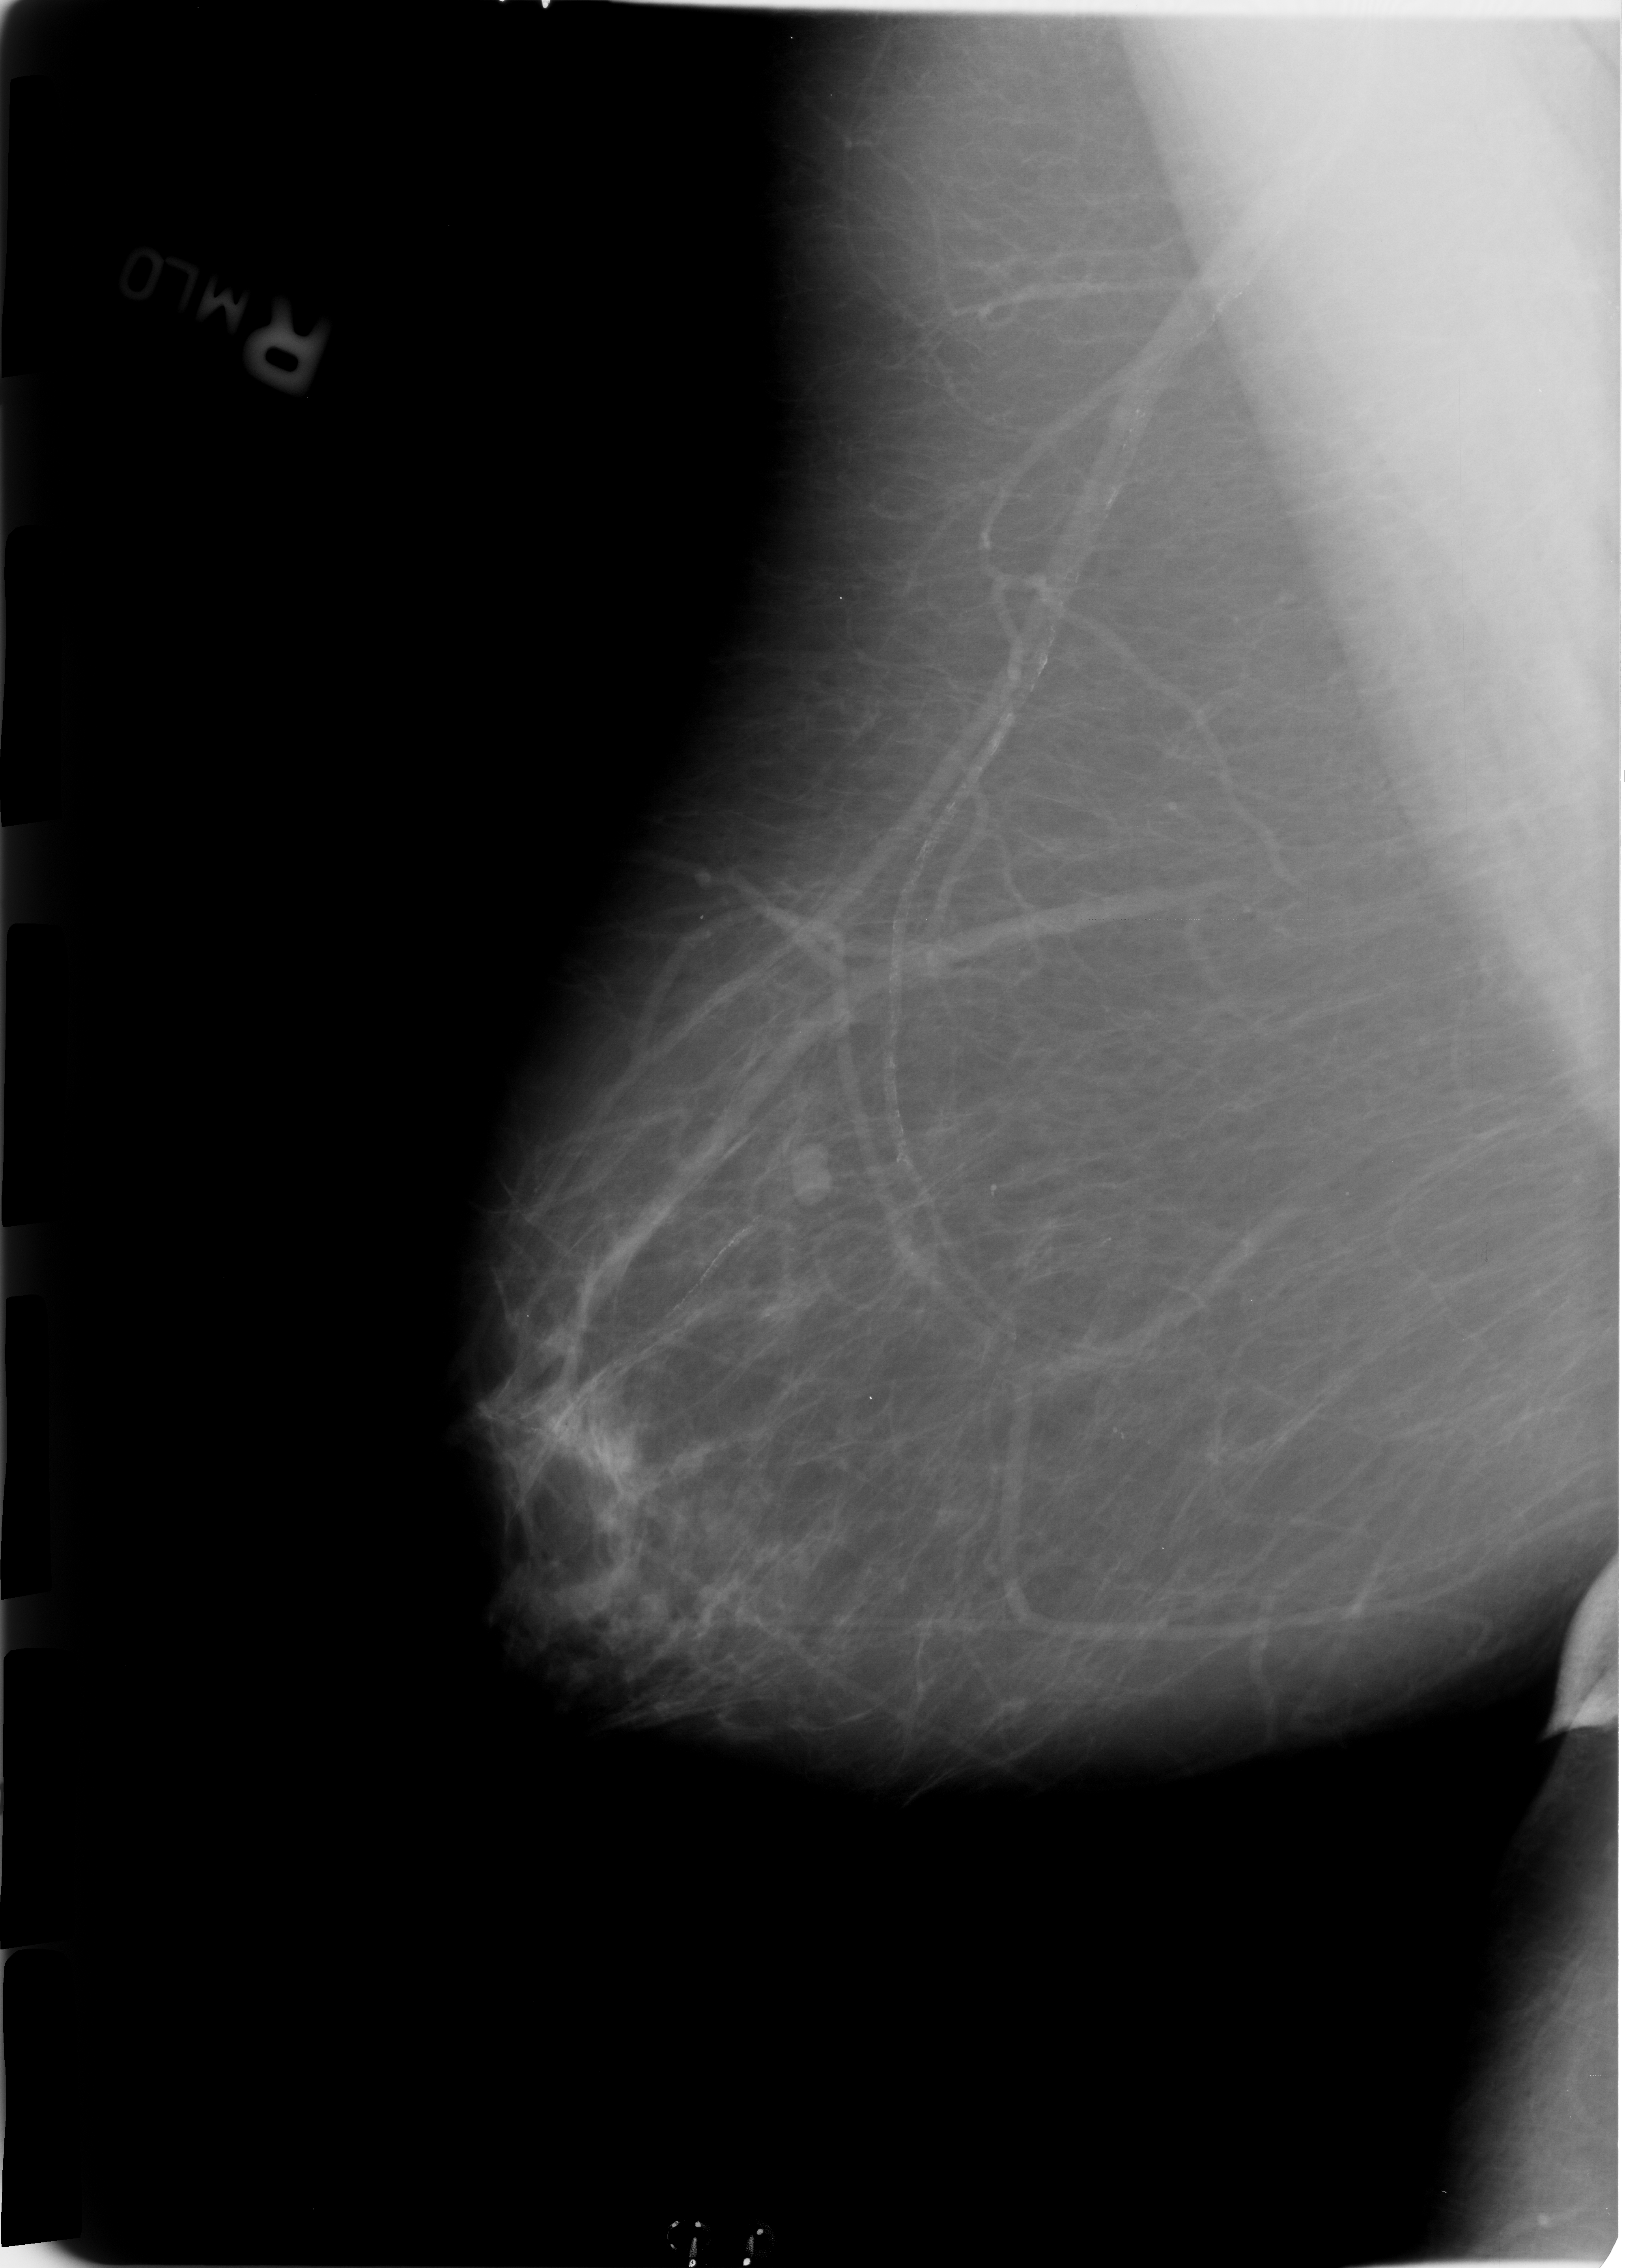
Scanned film-screen mammogram. Right breast. MLO view. Breast composition: scattered fibroglandular densities (BI-RADS density category 2 of 4). 1625 × 2268 image matrix.
Marked abnormalities (boxes around the expert regions of interest):
- mass, shape lobulated / lymph node, margins circumscribed; BI-RADS assessment category 2; outcome (as recorded, no biopsy): benign without callback (not worked up further): bounding box (x1, y1, x2, y2) in pixels: (770, 1132, 844, 1207)